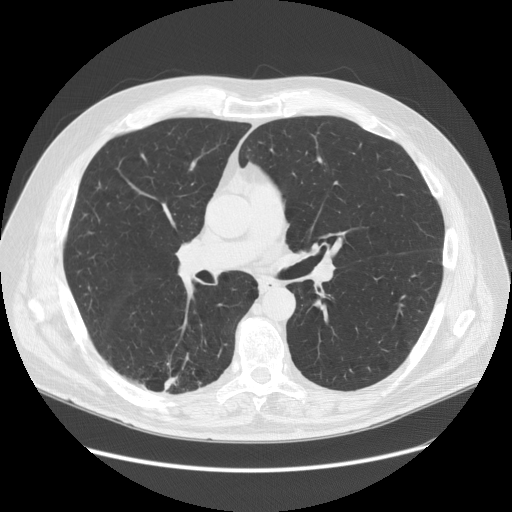
Low-dose screening chest CT, one axial slice. Position 81 of 149 along the scan axis. Lung window (W 1500 / L -600 HU). 2.5 mm slice thickness. 512 × 512 image matrix, field of view 400 × 400 mm.
Outlined on this slice (manually delineated by an expert):
- lesion 1 (tumor, lower lobe of right lung): bounding box [x1, y1, x2, y2] px = [163, 376, 177, 393]